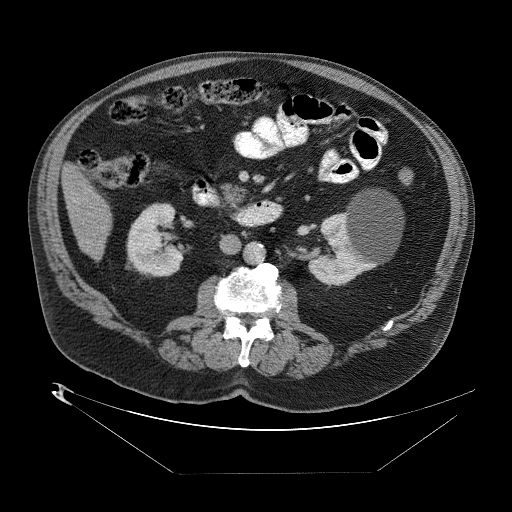
Contrast-enhanced abdominal CT (liver protocol), one axial slice. Position 12 of 89 along the scan axis. Reconstruction kernel STANDARD. 140 kVp. One of 2 acquisitions stored at this slice position. Soft-tissue window (W 400 / L 40 HU). 512 × 512 image matrix. Case-level facts recorded for this patient, not image findings: diagnosis: hepatocellular carcinoma (patient treated with transarterial chemoembolisation; whether this scan precedes or follows treatment is not stated here); TNM stage (as recorded): Stage-II; Child-Pugh class: B; tumour nodularity: multinodular; tumour size: 4 cm.
Outlined on this slice (semi-automatically segmented with operator editing):
- abdominal aorta: bounding box [x1, y1, x2, y2] px = [244, 243, 265, 266]
- liver parenchyma outside the tumour (the mass and vessels are separate outlines, so this box may not span the whole liver): [62, 165, 112, 256]
- liver vessels: [68, 190, 88, 248]